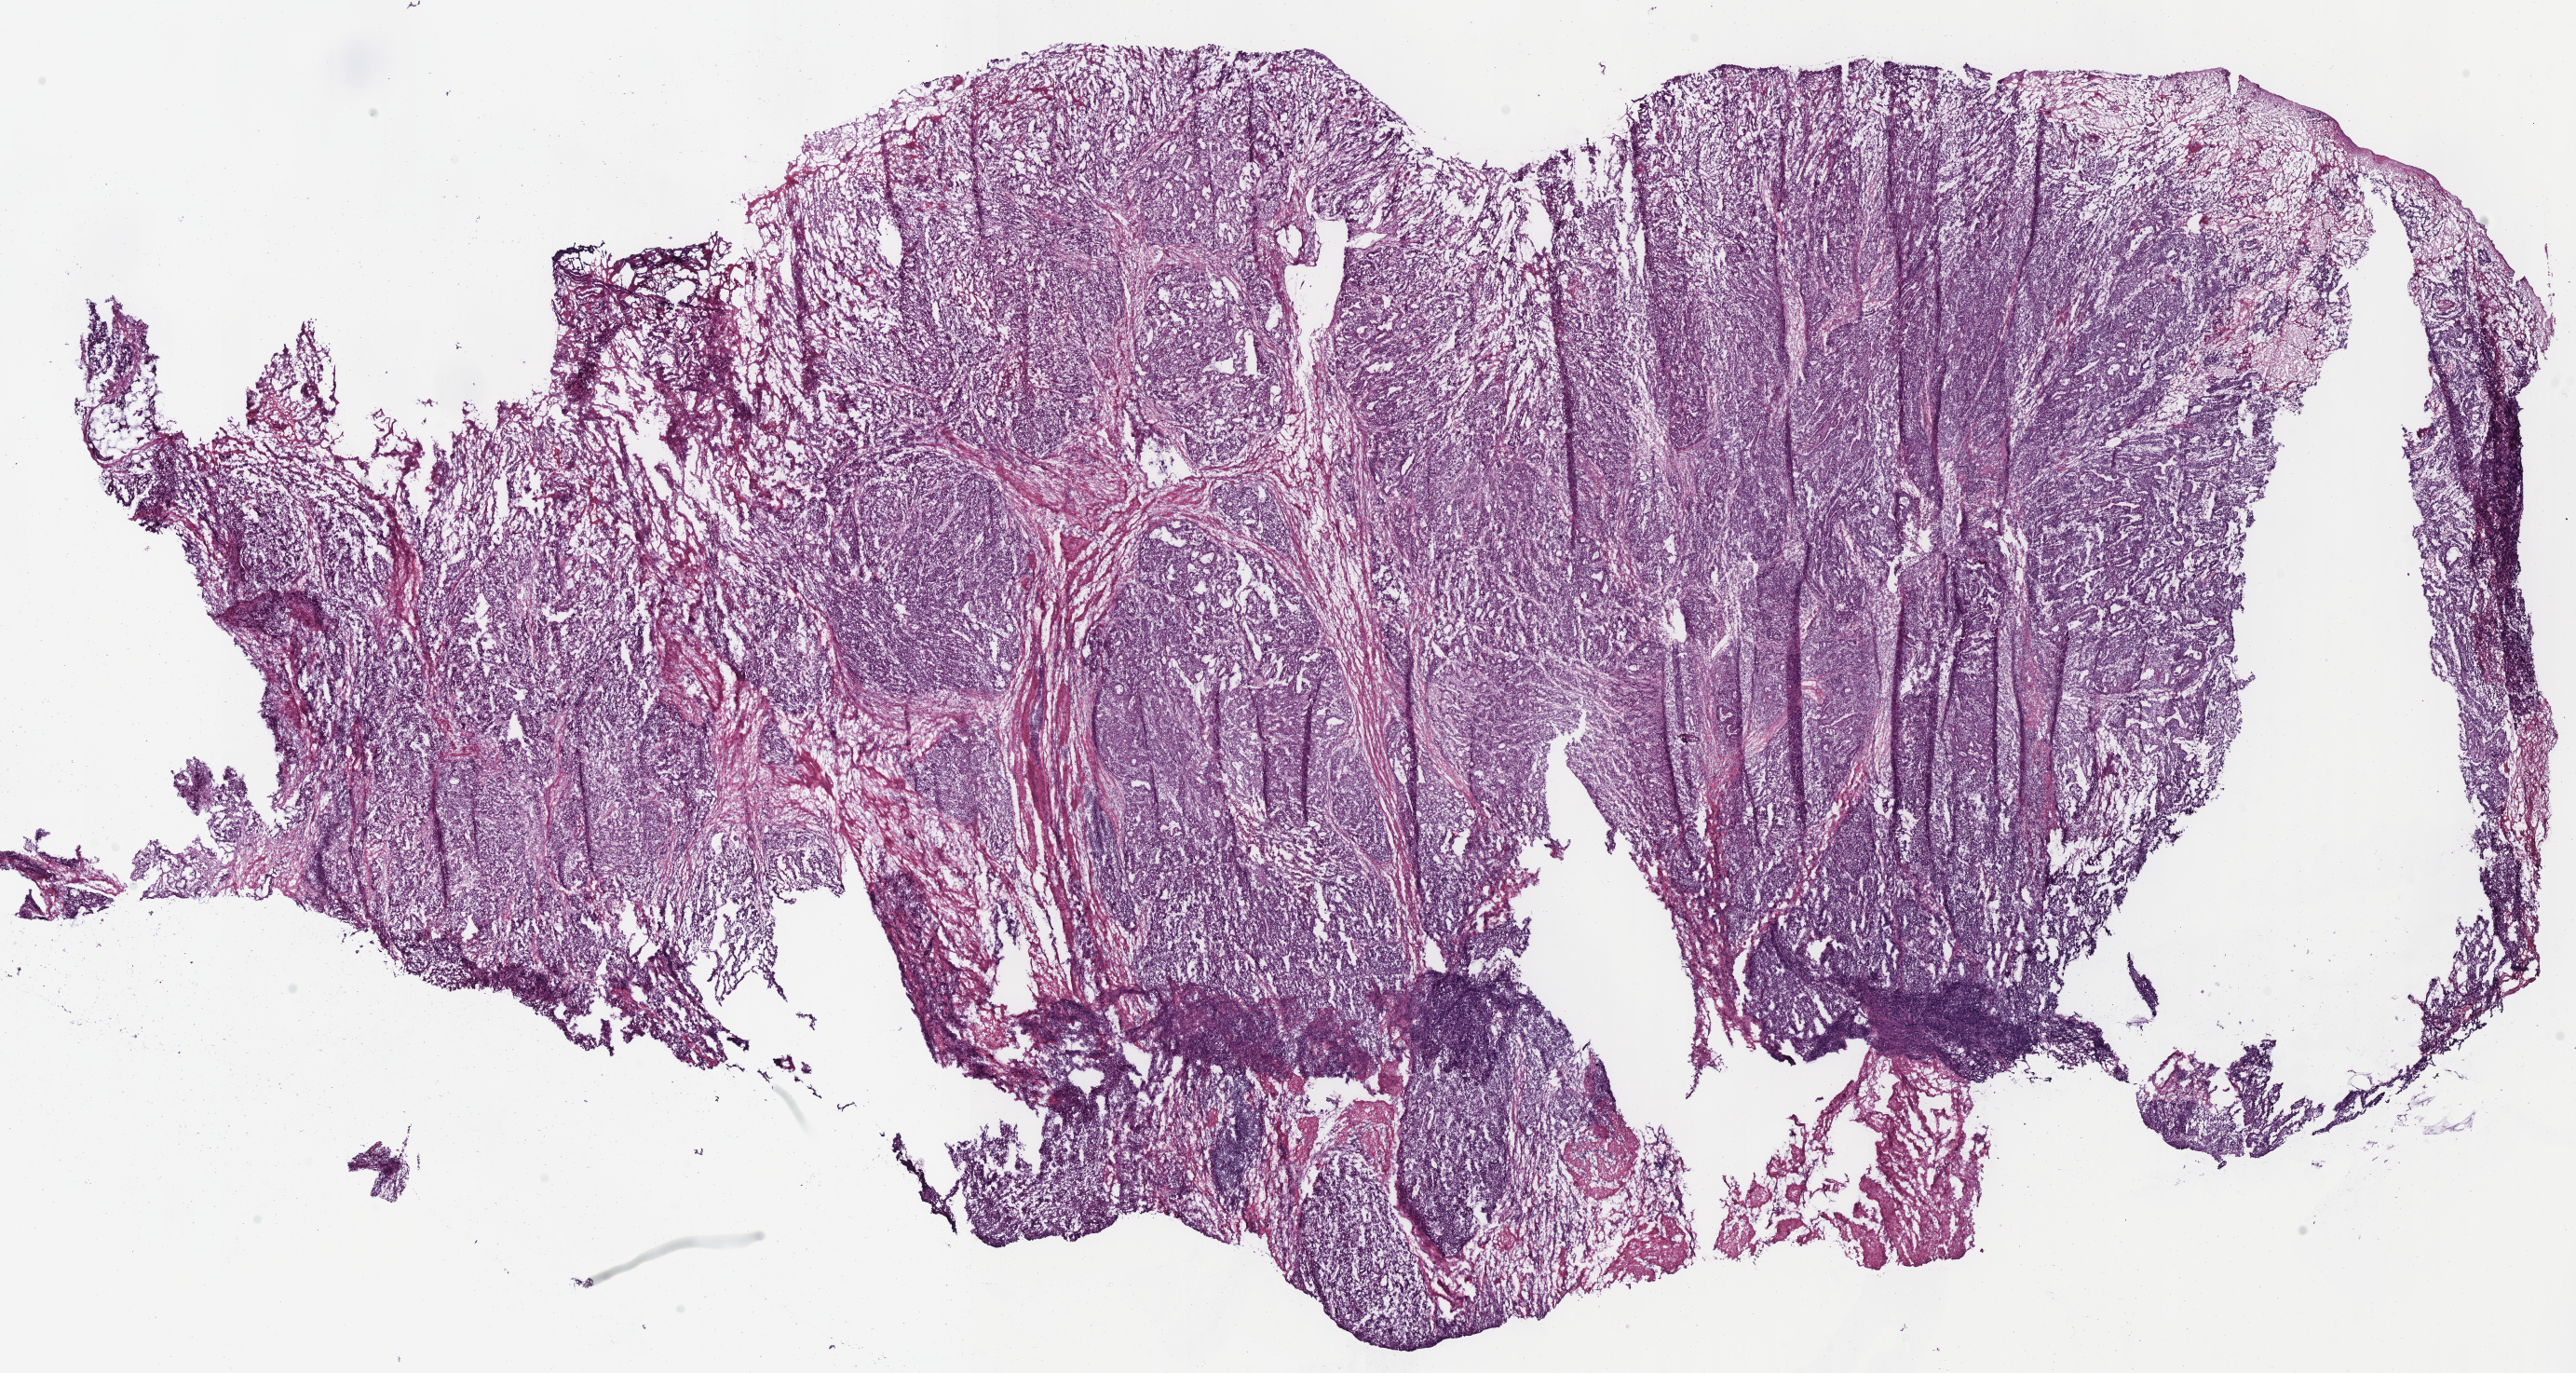
Whole-slide histology image, H&E — shown as a low-resolution overview of the whole scanned area (about 21.8 x 11.6 mm, from a 40x scan). Frozen section from the bottom of the tissue portion. Primary tumour sample from the stomach. Patient: male, age at initial diagnosis 63 years.
Pathologic diagnosis: Adenocarcinoma, intestinal type (fundus of stomach).